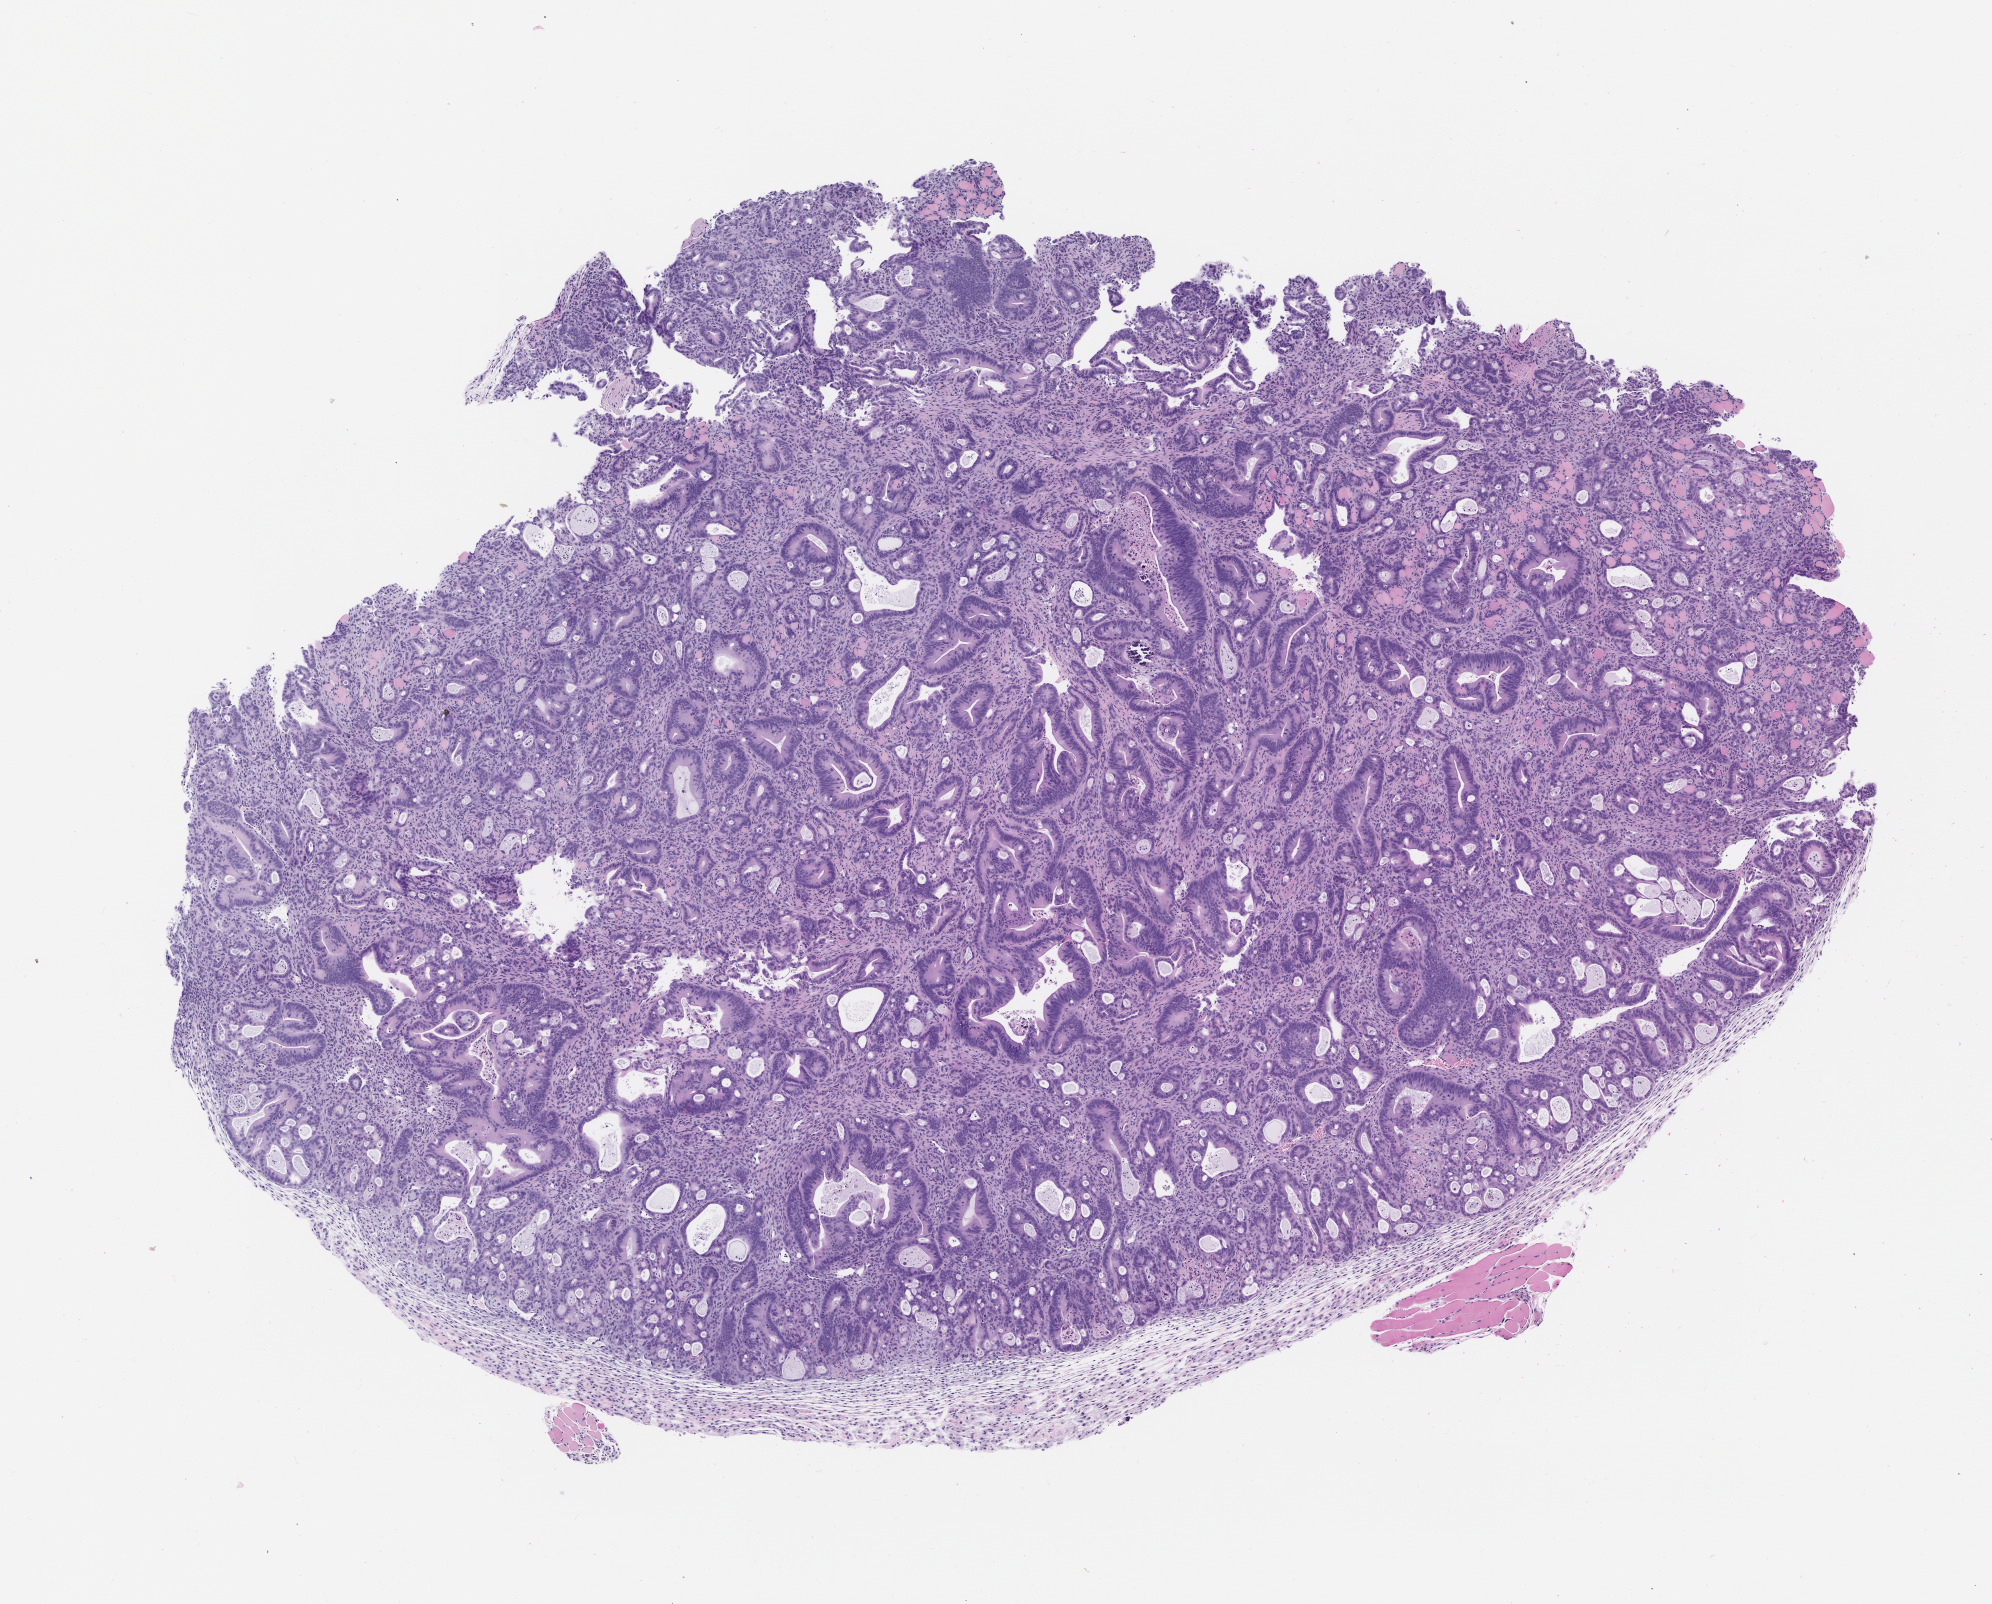
Whole-slide image, hematoxylin and eosin (H&E): patient-derived xenograft (human tumor grown in a mouse), passage 0 — low-resolution overview of the scanned area, about 8.0 x 6.5 mm; formalin-fixed paraffin-embedded section; tumor site category: colon.
Originating patient diagnosis: Colon Adenocarcinoma.